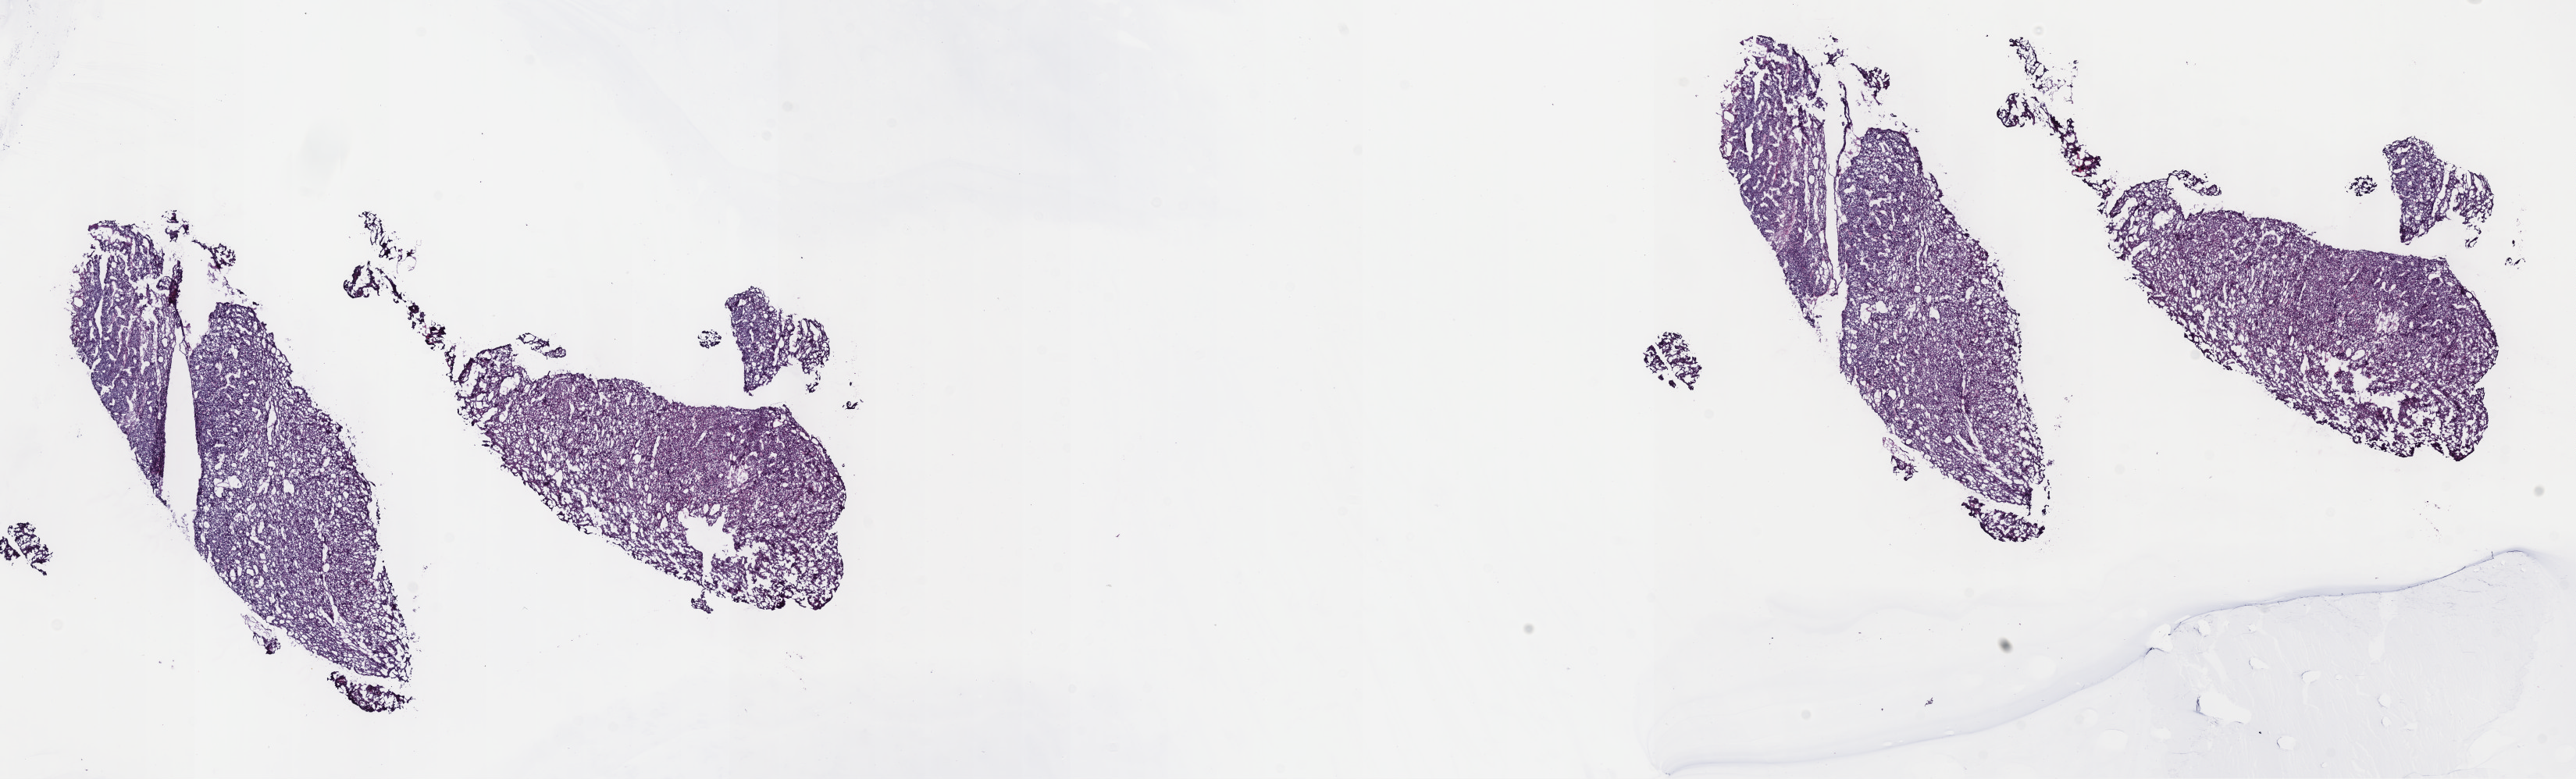
Hematoxylin and eosin (H&E) stained whole-slide image — low-resolution overview of the scanned area, about 26.7 x 8.1 mm (from a 40x scan); frozen section from the top of the tissue portion; sample: primary tumour, thymus. Patient: female, age at initial diagnosis 81 years. Slide review estimates, as recorded: tumour cells 100%, tumour nuclei 80%, normal cells 0%, stromal cells 0%, necrosis 0%. Infiltration values recorded for this section: lymphocyte infiltration 1%, monocyte infiltration 1%, neutrophil infiltration 0%.
Diagnosis: Thymoma, type AB, malignant.